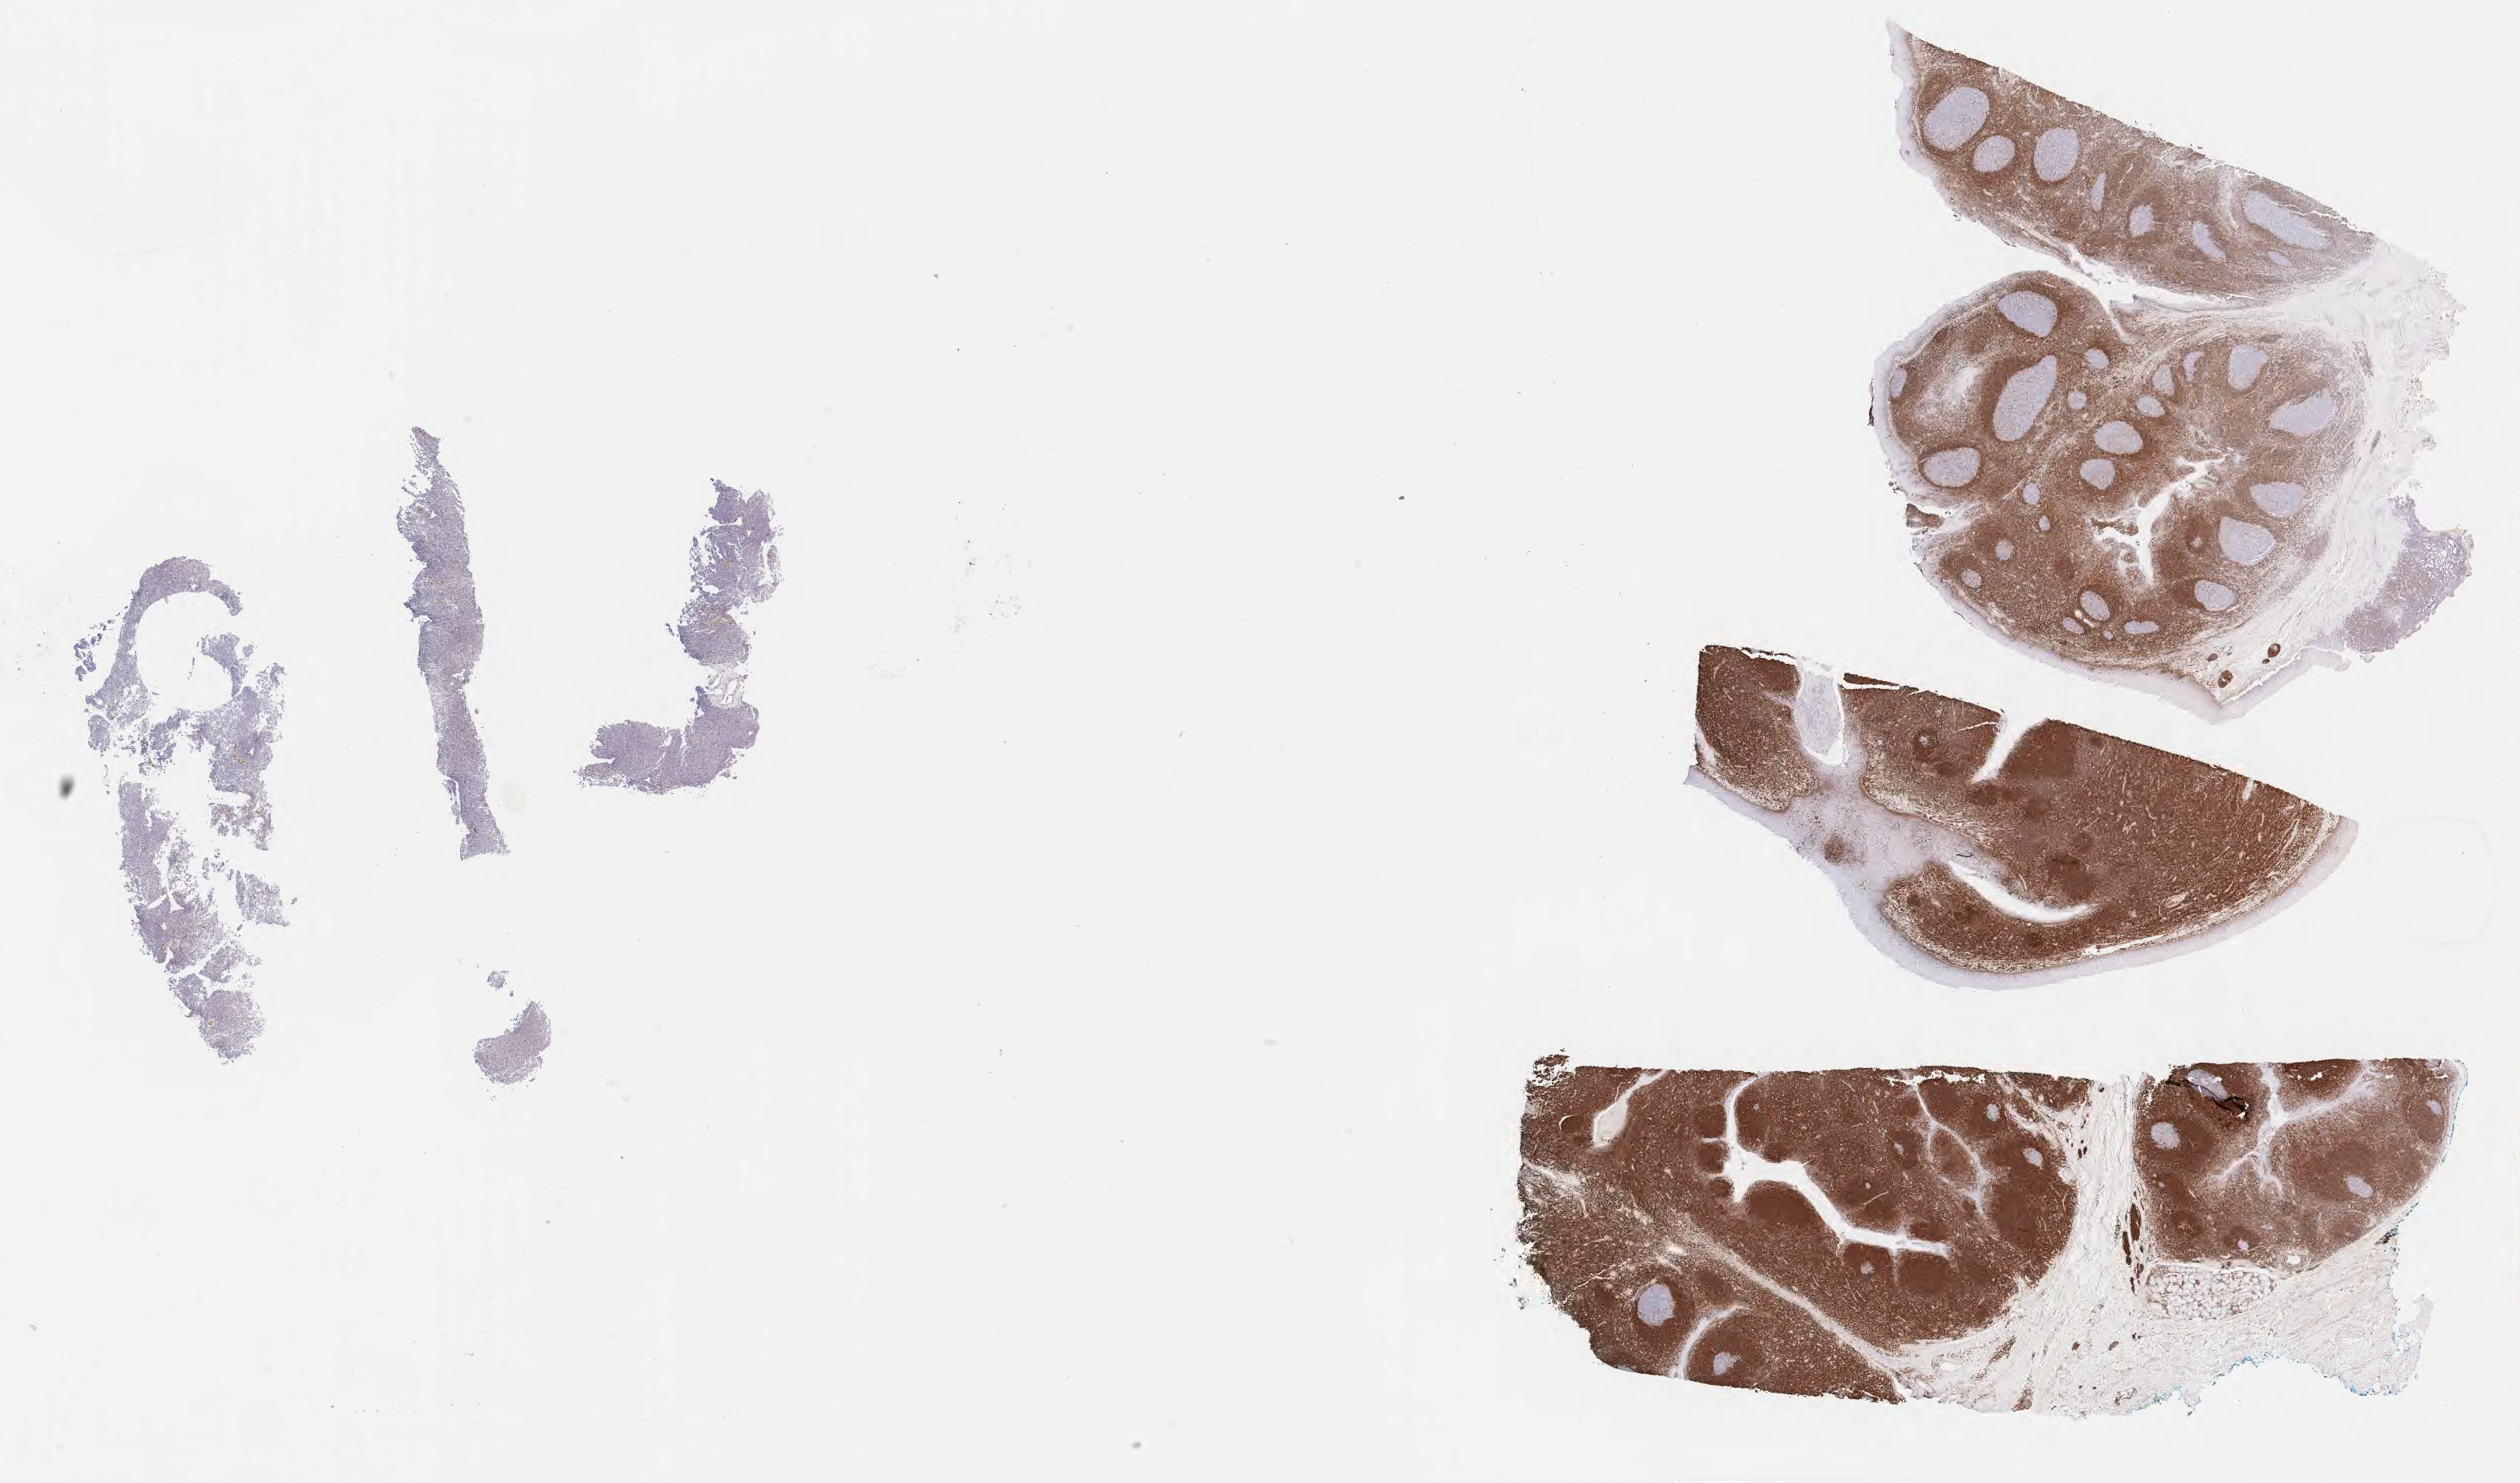
Immunohistochemistry (IHC) whole-slide image stained for BCL2 — low-resolution overview of the scanned area, about 26.2 x 15.4 mm. Tumor tissue. Anatomic site: spleen. Male patient; age at initial diagnosis 8 years.
Histologic diagnosis: Burkitt lymphoma, NOS.